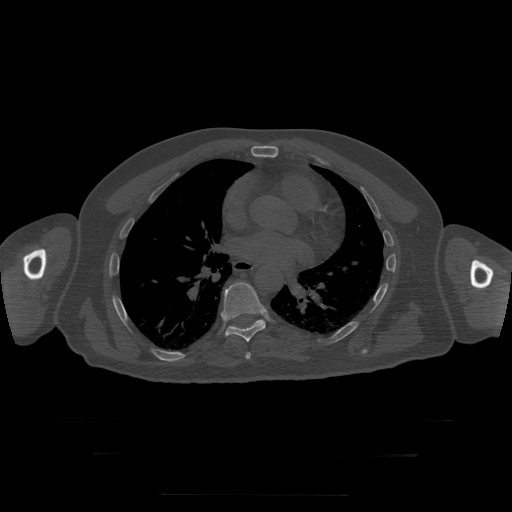
CT including the spine, one axial slice; position 164 of 397 along the scan axis; 120 kVp; bone window (W 1800 / L 400 HU); 512 × 512 image matrix. Patient age 73 years. Case-level facts recorded for this patient, not image findings: primary cancer: prostate.
Structures marked on this image (semi-automatically segmented with operator editing):
- T7 vertebra: bounding box [x1, y1, x2, y2] px = [246, 353, 251, 360]
- T8 vertebra: [221, 282, 266, 342]
- T9 vertebra: [233, 320, 264, 328]